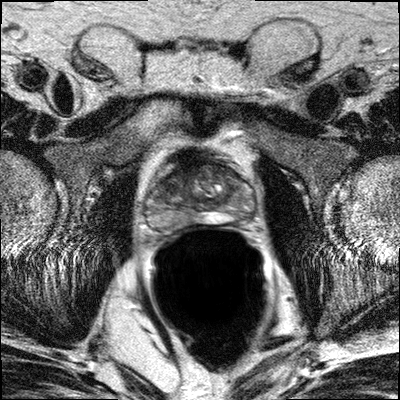
MRI of the prostate; 3 images, each a single mid-volume slice chosen by position (not for content).
Image 1: T2-weighted axial slice, series "T2W_TSE_AX", slice 17 of 32, 3 mm slice thickness.
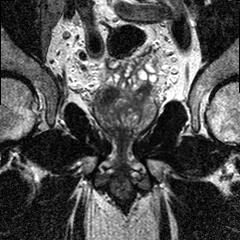
Image 2: T2-weighted coronal slice, series "T2W_TSE_COR", slice 13 of 24, 3 mm slice thickness.
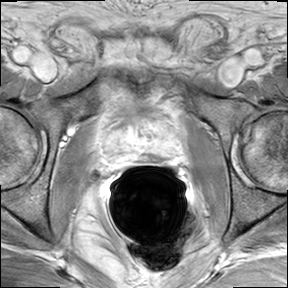
Image 3: DCE (dynamic gadolinium-enhanced) axial slice, series "AX BLISS_GAD_8", slice 17 of 32, dynamic phase 5 of 8.
Radiologist's MRI report for this examination:
The prostate anatomy is preserved. Maximal transverse diameter of 4.5, maximal AP diameter 2.7, maximal CC diameter 3.9. Estimated gland volume 25 cc. There is signs for the BPH and chronic prostatitis. In the right paramedian posterior peripheral zone of the mid 3rd of the prostate between 6 and 7 o'clock there is an elongated area measuring 9 x 3 mm of up hypointense T2-W signal seen with rapid wash-in and wash-out on the dynamic series. Otherwise, there is only diffuse T2 weighted signal alteration, seen, with perseveration of centrifugal "pseudo septations", in general heterogenous signal on T2, with corresponding centrifugal fine linear enhancement, suggestive for chronic prostatitis. No evidence of capsular indication or extra glandular extension. Both neurovascular bundles are uninvolved. No seminal vesicles infiltration. Bilateral there are small morphologically benign appearing lymph node seen along the internal iliac vessels; no evidence of pelvic the lymphadenopathy. IMPRESSION: Prostate cancer on the right, with dominant nodule in the posterior lateral peripheral zone between 6-7 o'clock, mid third of the prostate; on the background of chronic prostatitis small additional foci on the right or on the left cannot be excluded. There is no capsular infiltration or extraglandular extension. Unremarkable neurovascular bundles (based on imaging findings, bilateral nerve sparing possible). No evidence of seminal vesicle infiltration; no evidence of pelvic lymphadenopathy.

Biopsy pathology report for this patient (as recorded):
PROSTATE BIOPSY: 1. RIGHT PZ PROSTATIC ADENOCARCINOMA (GLEASON SCORE 3+3=6/10, INVOLVING ONE CORE AND LESS THAN 2% OF TISSUE. PIN-4 STAIN CONFIRMS DIAGNOSIS. ACUTE AND CHRONIC PROSTATITIS. 2. RIGHT PZ/TZ: BENIGN PROSTATIC TISSUE WITH ACUTE AND CHRONIC PROSTATITIS 3. RIGHT APEX: BENIGN PROSTATIC TISSUE WITH CHRONIC PROSTATITIS. 4. LEFT PZ: BENIGN PROSTATIC TISSUE WITH CHRONIC PROSTATITIS. 5. LEFT PZ/TZ BENIGN PROSTATIC TISSUE WITH CHRONIC PROSTATITIS. 6. LEFT APEX: BENIGN PROSTATIC TISSUE WITH ACUTE AND CHRONIC PROSTATITIS.